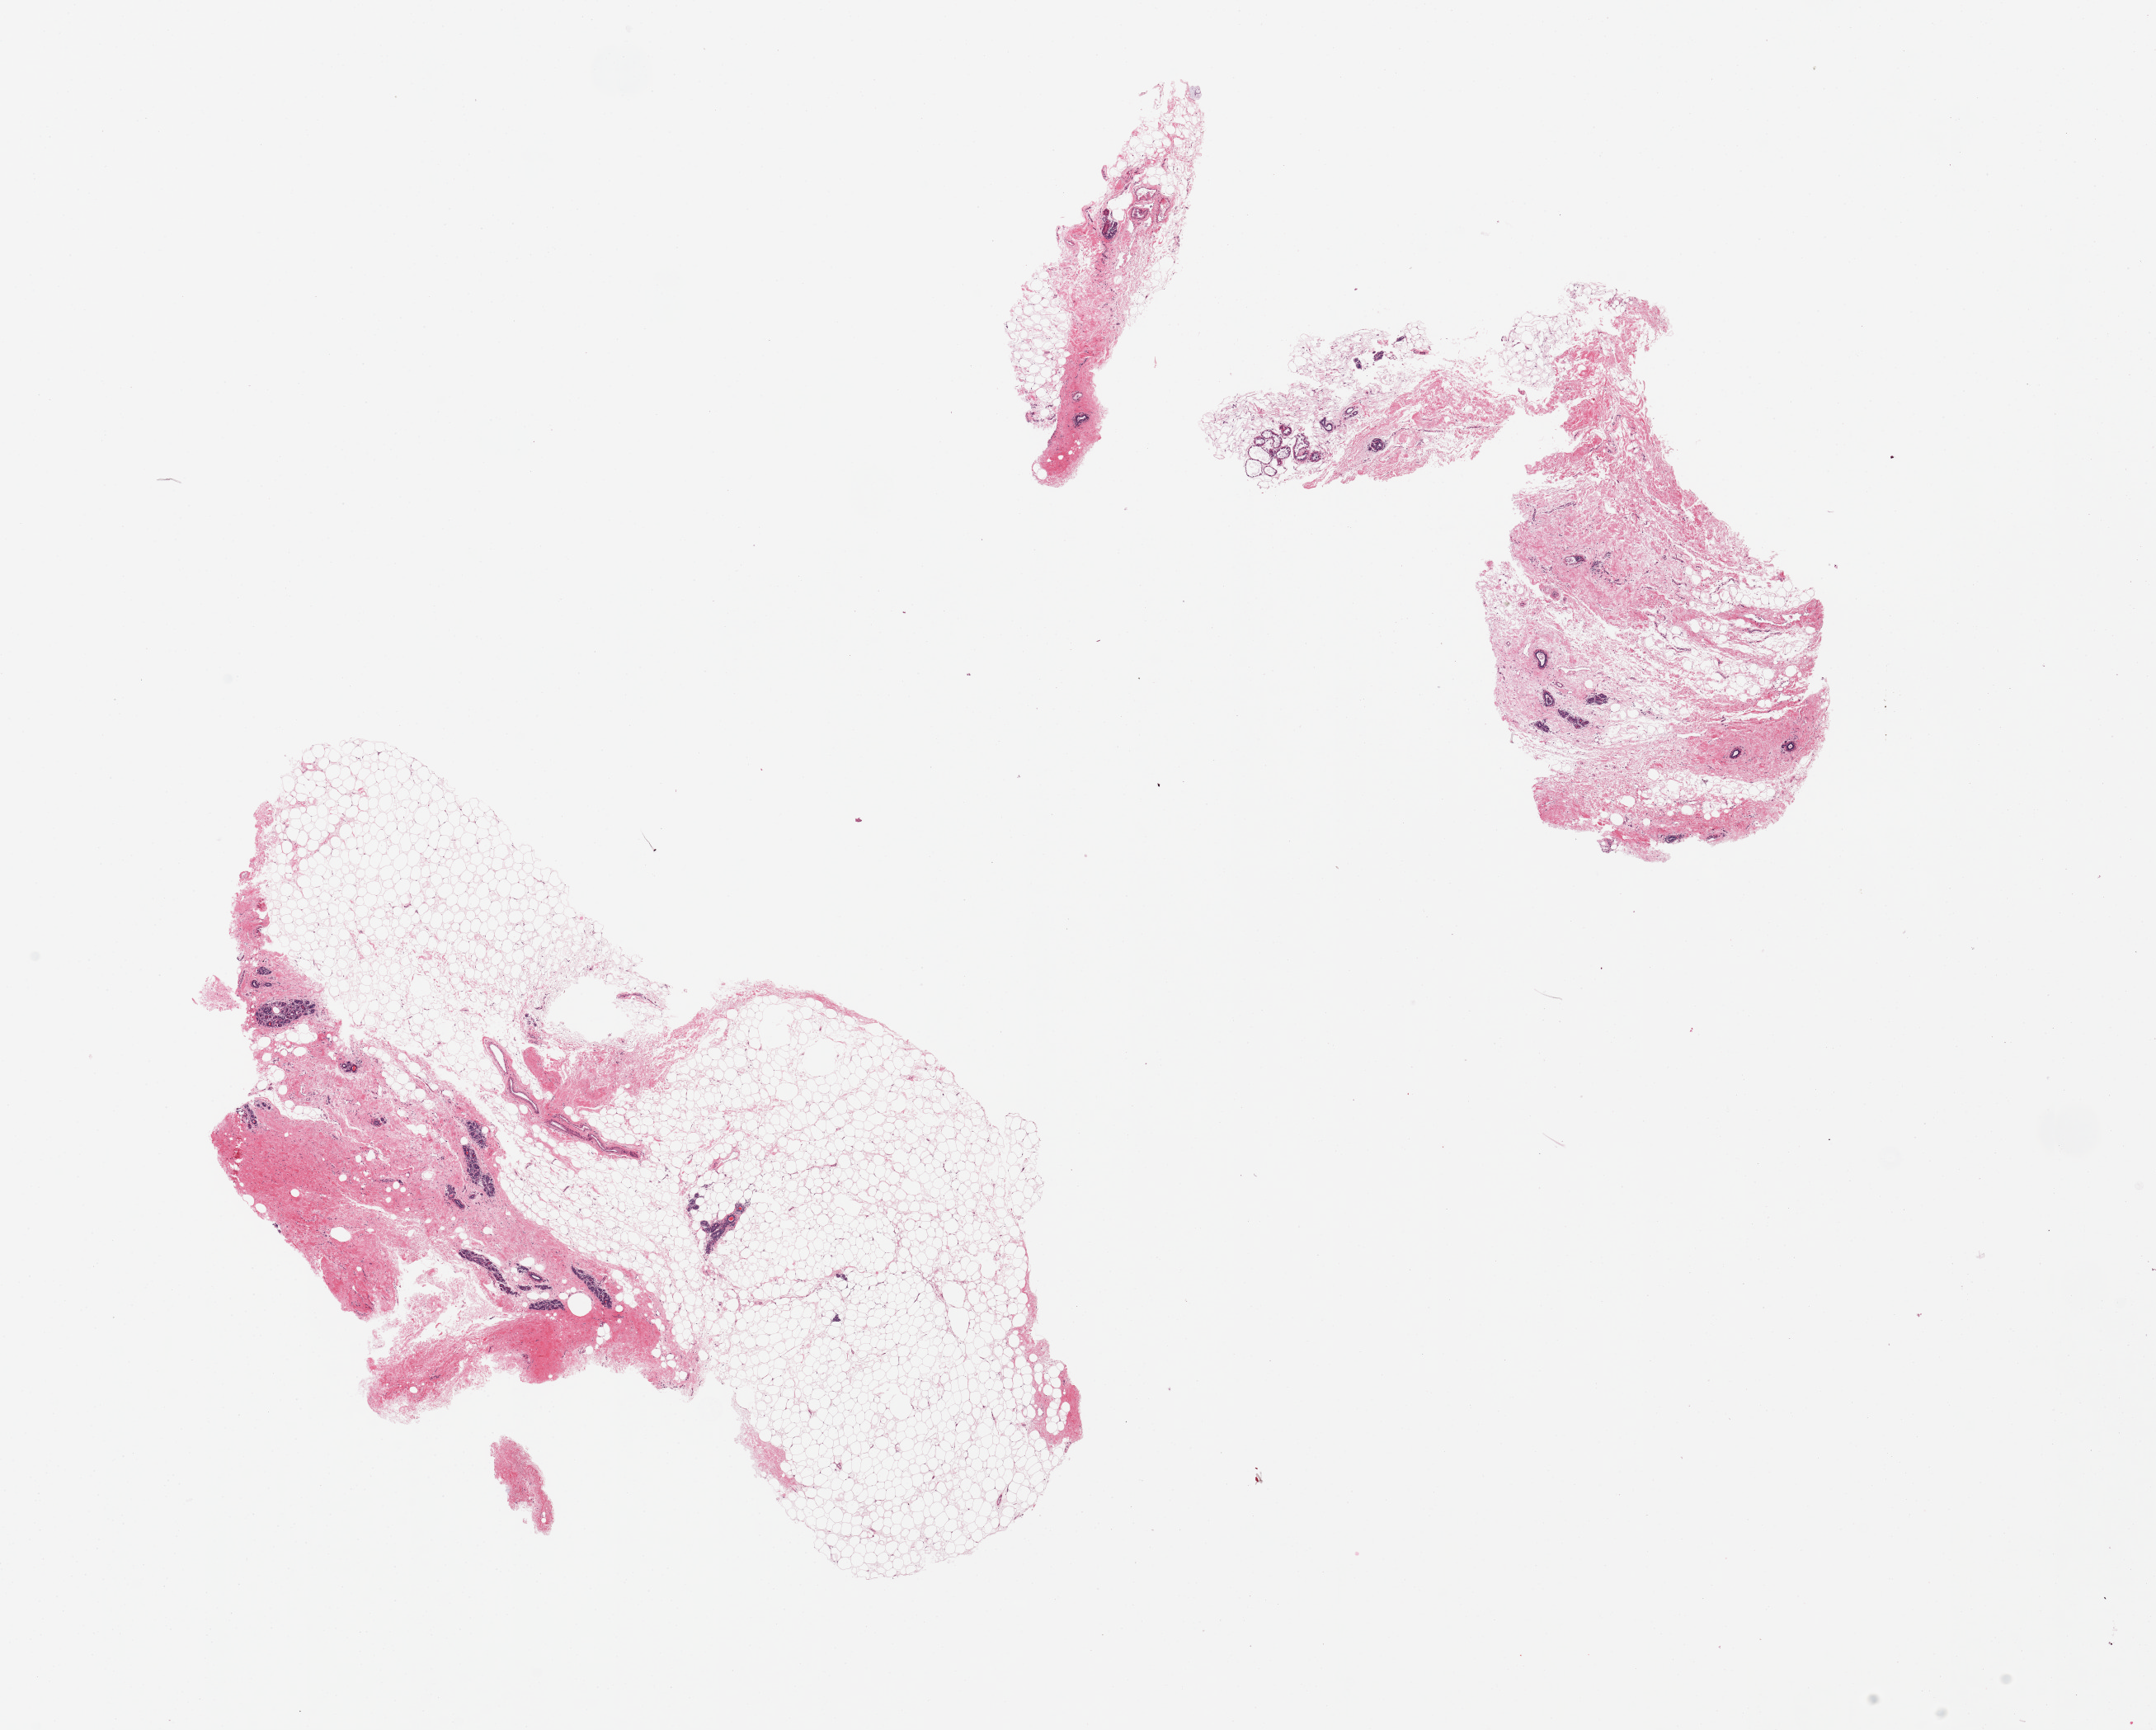
Digitized haematoxylin and eosin-stained section — whole scanned area (about 20.7 x 16.6 mm) shown as a low-resolution overview. PAXgene-fixed, paraffin-embedded tissue. Section of breast (target tissue). Donor tissue sample. Donor sex: female.
Pathologist's review note for this sample: 2 pieces, atrophic duct lobular units; Focal secretory metaplasia; Abundant fat, normal post-menopausal atrophy.